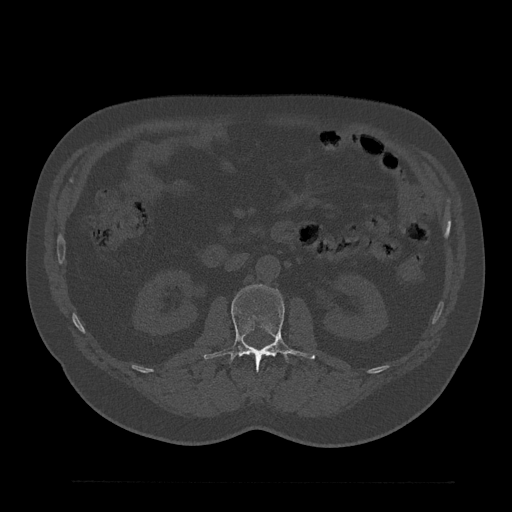
CT including the spine, one axial slice. Slice 102 of 797 in the series (ordered by position). Reconstruction kernel Br40s/3. Bone window (W 1800 / L 400 HU). 0.5 mm slice thickness. 512 × 512 image matrix, field of view 430 × 430 mm. Patient: male, 61 years. From the clinical record (not read from this slice): primary cancer: prostate.
Structures marked on this image (semi-automatic segmentation, software-assisted and operator-edited):
- L2 vertebra: bounding box <204,285,316,369> (left, top, right, bottom; pixels)